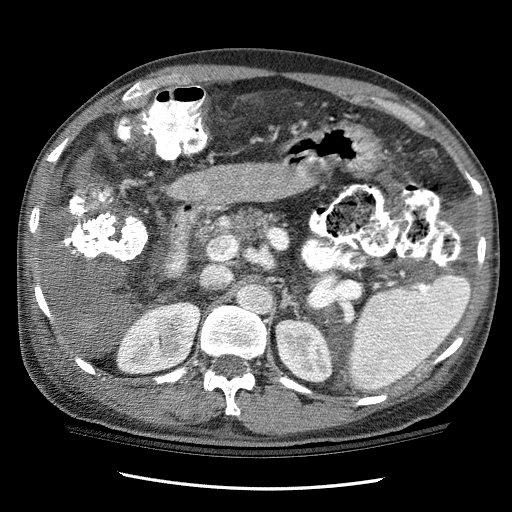
Contrast-enhanced abdominal CT (liver protocol), one axial slice. Reconstruction kernel STANDARD. One of 3 acquisitions stored at this slice position. Soft-tissue window (W 400 / L 40 HU). 2.5 mm slice thickness. 512 × 512 image matrix, field of view 360 × 360 mm. Case-level facts recorded for this patient, not image findings: diagnosis: hepatocellular carcinoma (patient treated with transarterial chemoembolisation; whether this scan precedes or follows treatment is not stated here); TNM stage (as recorded): Stage-I; Child-Pugh class: C; tumour nodularity: uninodular.
Outlined on this slice (semi-automatic segmentation, software-assisted and operator-edited):
- liver parenchyma outside the tumour (the mass and vessels are separate outlines, so this box may not span the whole liver): bounding box (x1, y1, x2, y2) in pixels: (170, 162, 313, 207)